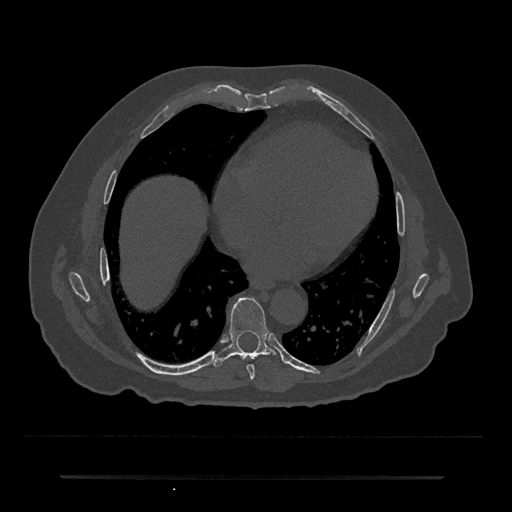
CT including the spine, one axial slice. Reconstruction kernel Br40s/3. 120 kVp. Bone window (W 1800 / L 400 HU). 0.5 mm slice thickness. 512 × 512 image matrix, field of view 437 × 437 mm. Male patient, age 69 years. Case-level facts recorded for this patient, not image findings: primary cancer: prostate.
Structures marked on this image (semi-automatically segmented with operator editing):
- T7 vertebra: bounding box (x1, y1, x2, y2) in pixels: (246, 364, 255, 379)
- T8 vertebra: (213, 297, 280, 367)